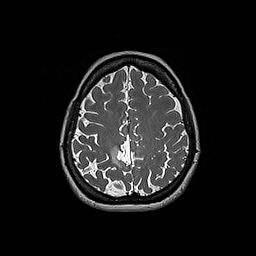
Brain MRI from a brain-tumour surgery series, one axial slice. Slice 58 of 192 in the series (ordered by position). 256 × 256 image matrix, field of view 250 × 250 mm. Case-level facts recorded for this patient, not image findings: histopathology: Oligodendroglioma; WHO grade: 2; IDH mutation: yes.
Annotated regions visible in this slice (manually delineated by an expert):
- tumour: bounding box [x1, y1, x2, y2] px = [111, 146, 120, 167]